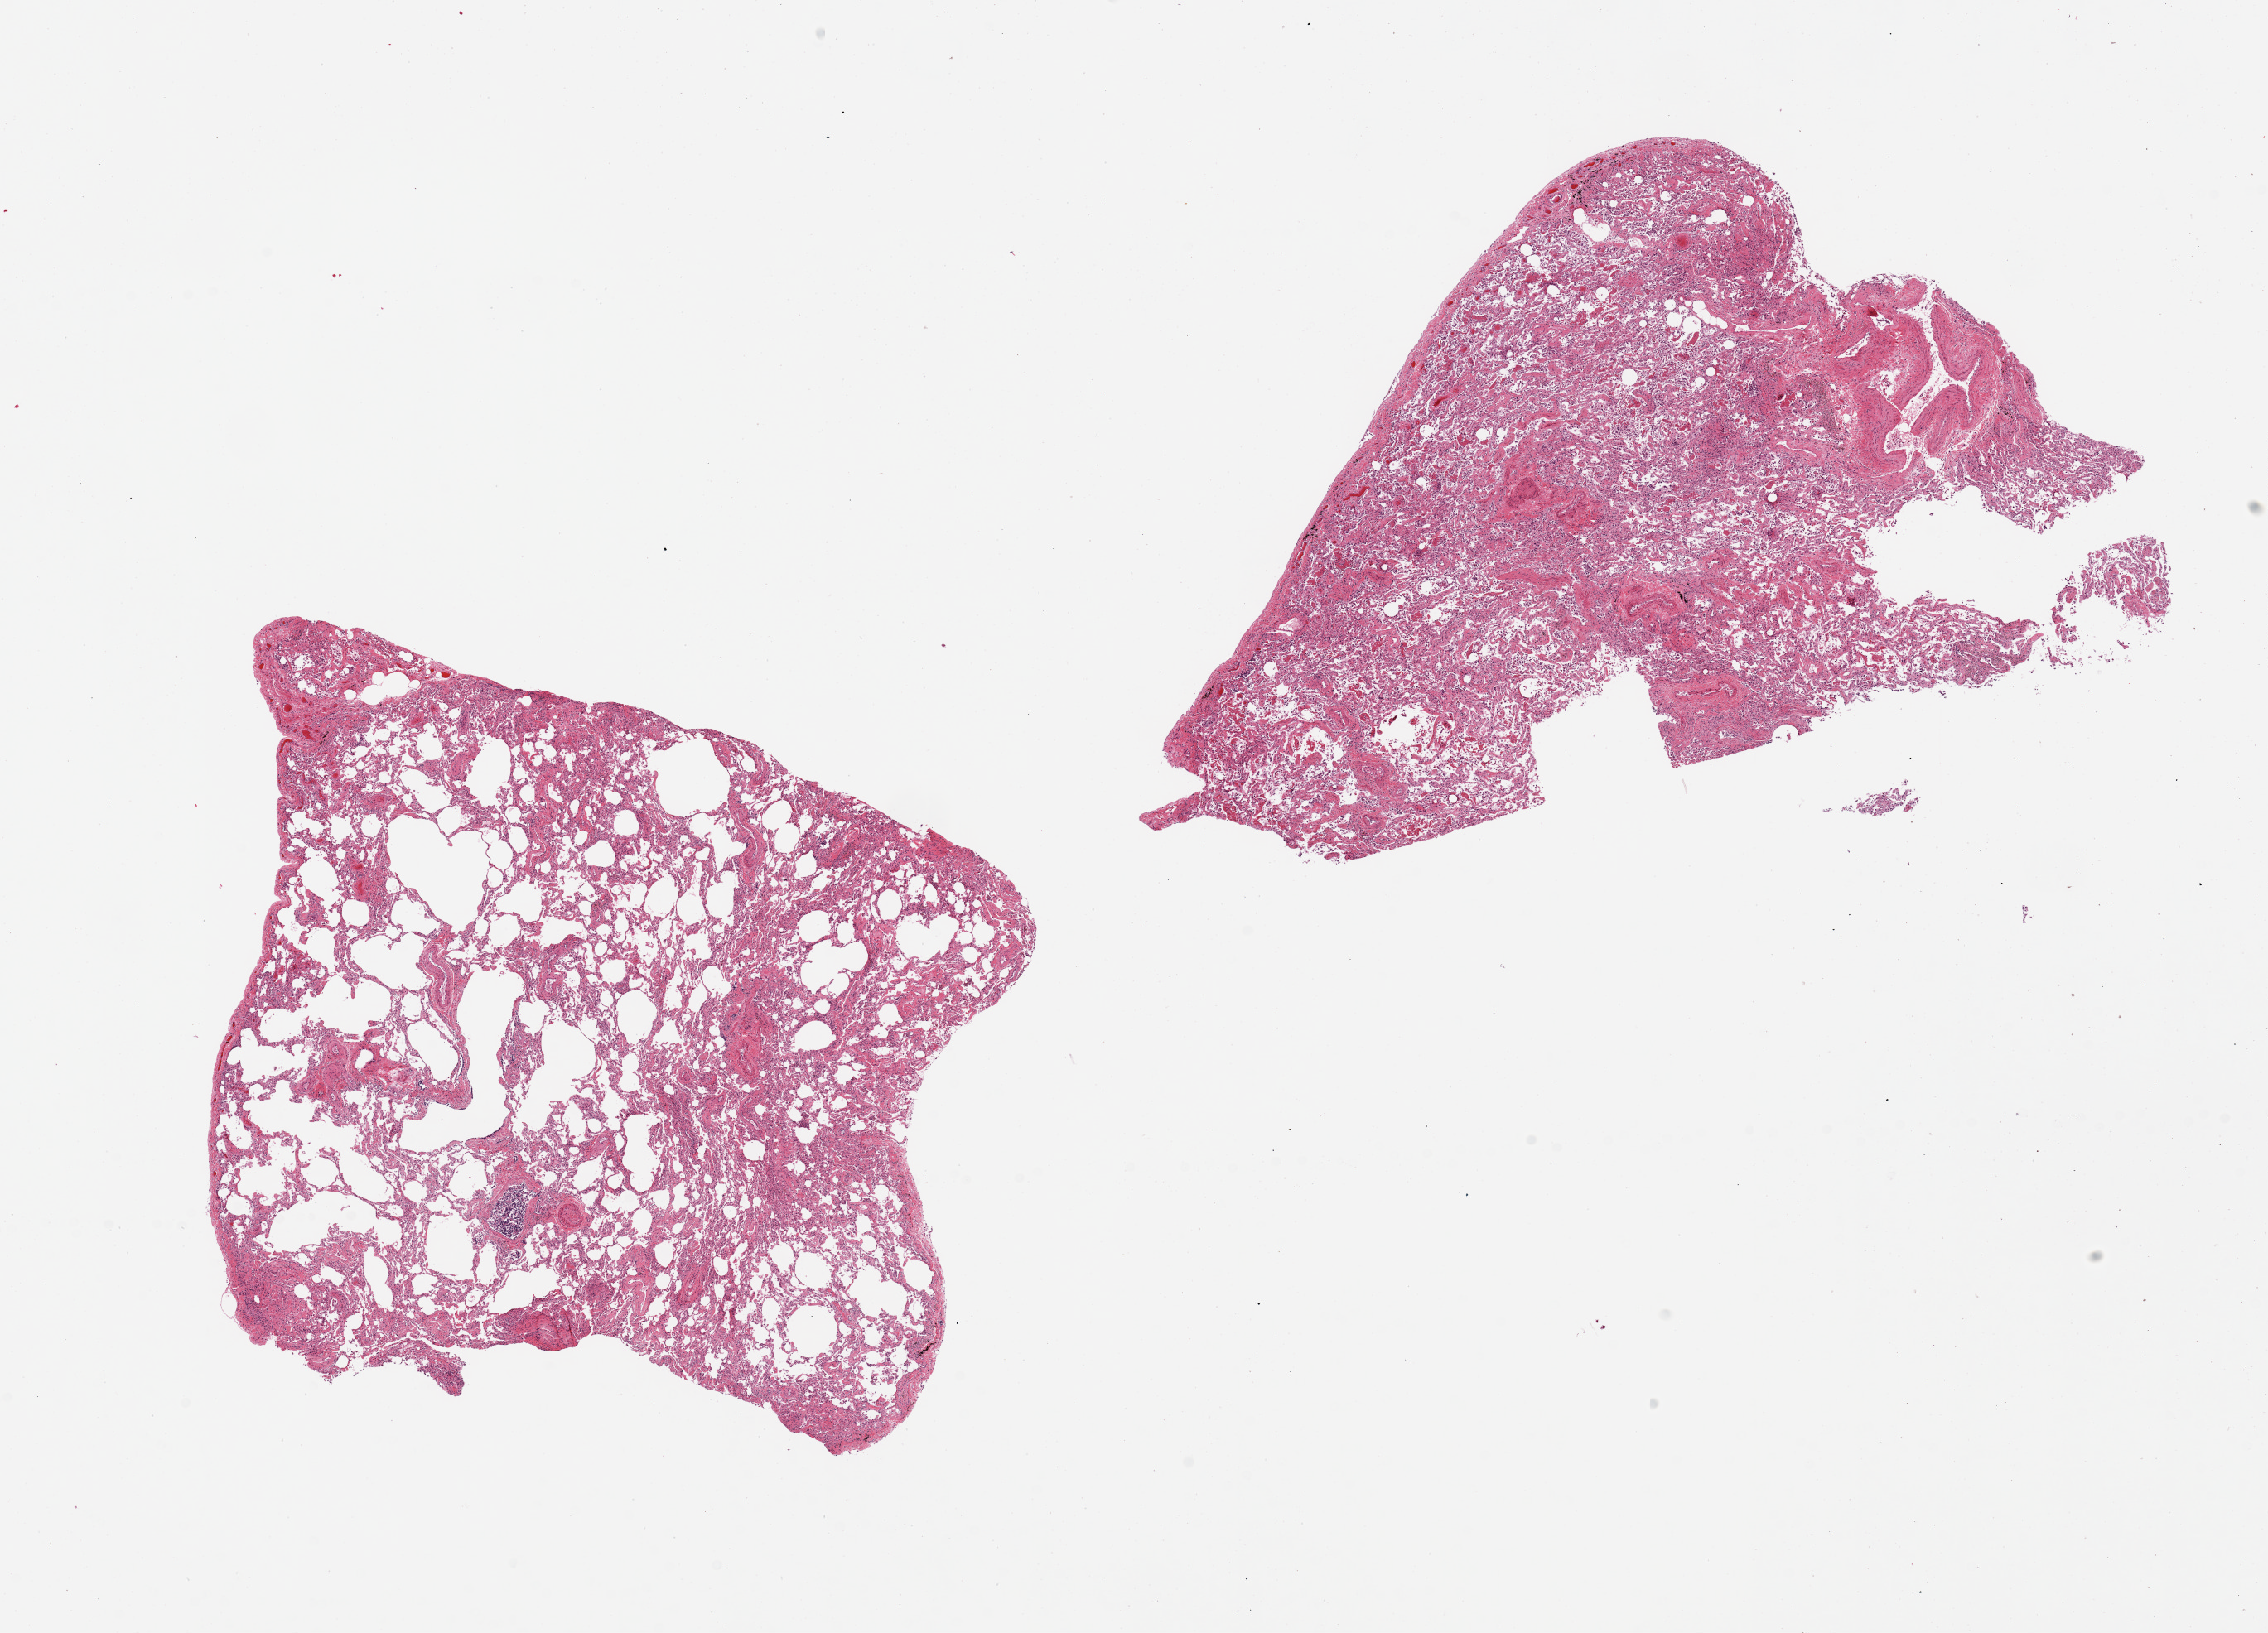
Whole-slide image, hematoxylin and eosin (H&E) stain, whole scanned area (about 21.7 x 15.6 mm, from a 20x scan) shown as a low-resolution overview; PAXgene-fixed, paraffin-embedded tissue; section of lung (target tissue); donor tissue sample. Donor: male.
Review note (as recorded): 2 pieces, one piece with emphysema-like change; the second piece with interstitial fibrosis, congestion, numerous hemsiderin-laden macrophages and chronic inflammation.